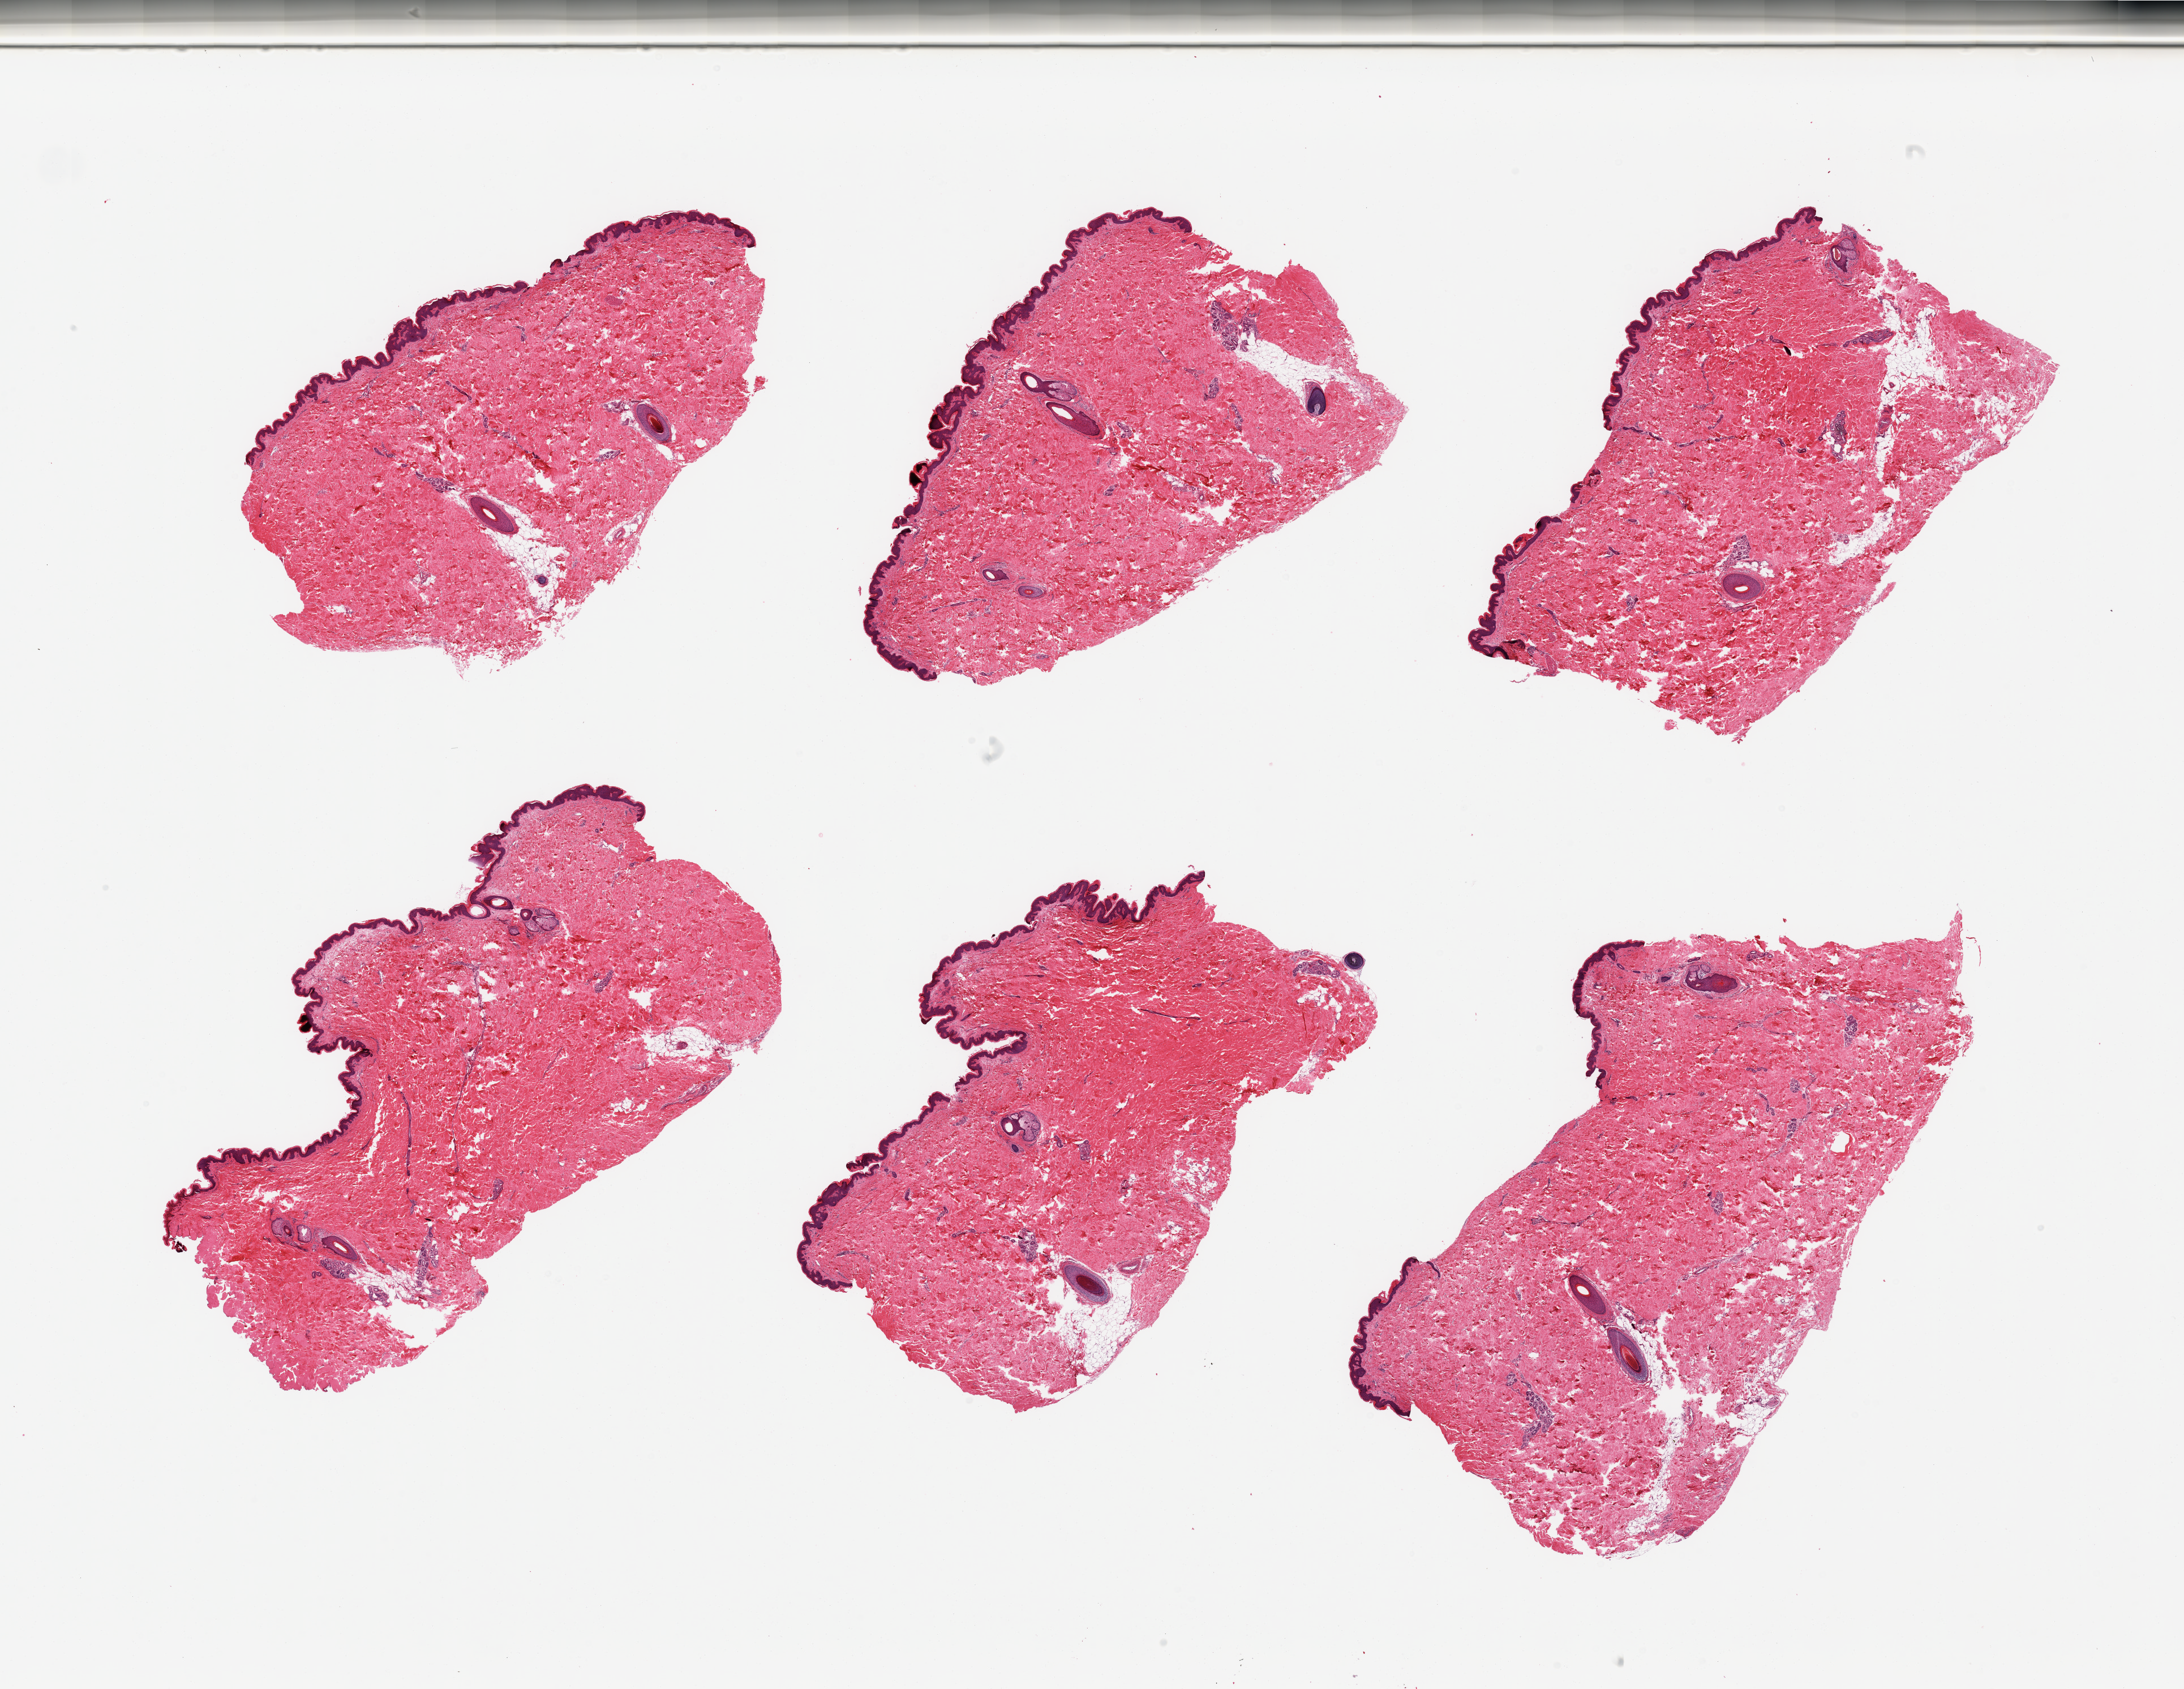
Haematoxylin and eosin whole-slide image, shown as a low-resolution overview of the whole scanned area (about 30.5 x 23.6 mm), PAXgene-fixed paraffin-embedded (PFPE) section, sampled site (target tissue): skin of suprapubic region, donor tissue sample. Donor sex: male.
- pathologist's review note for this sample: 6 pieces, trace dermal fat; squamous epithelium is ~50-60 microns